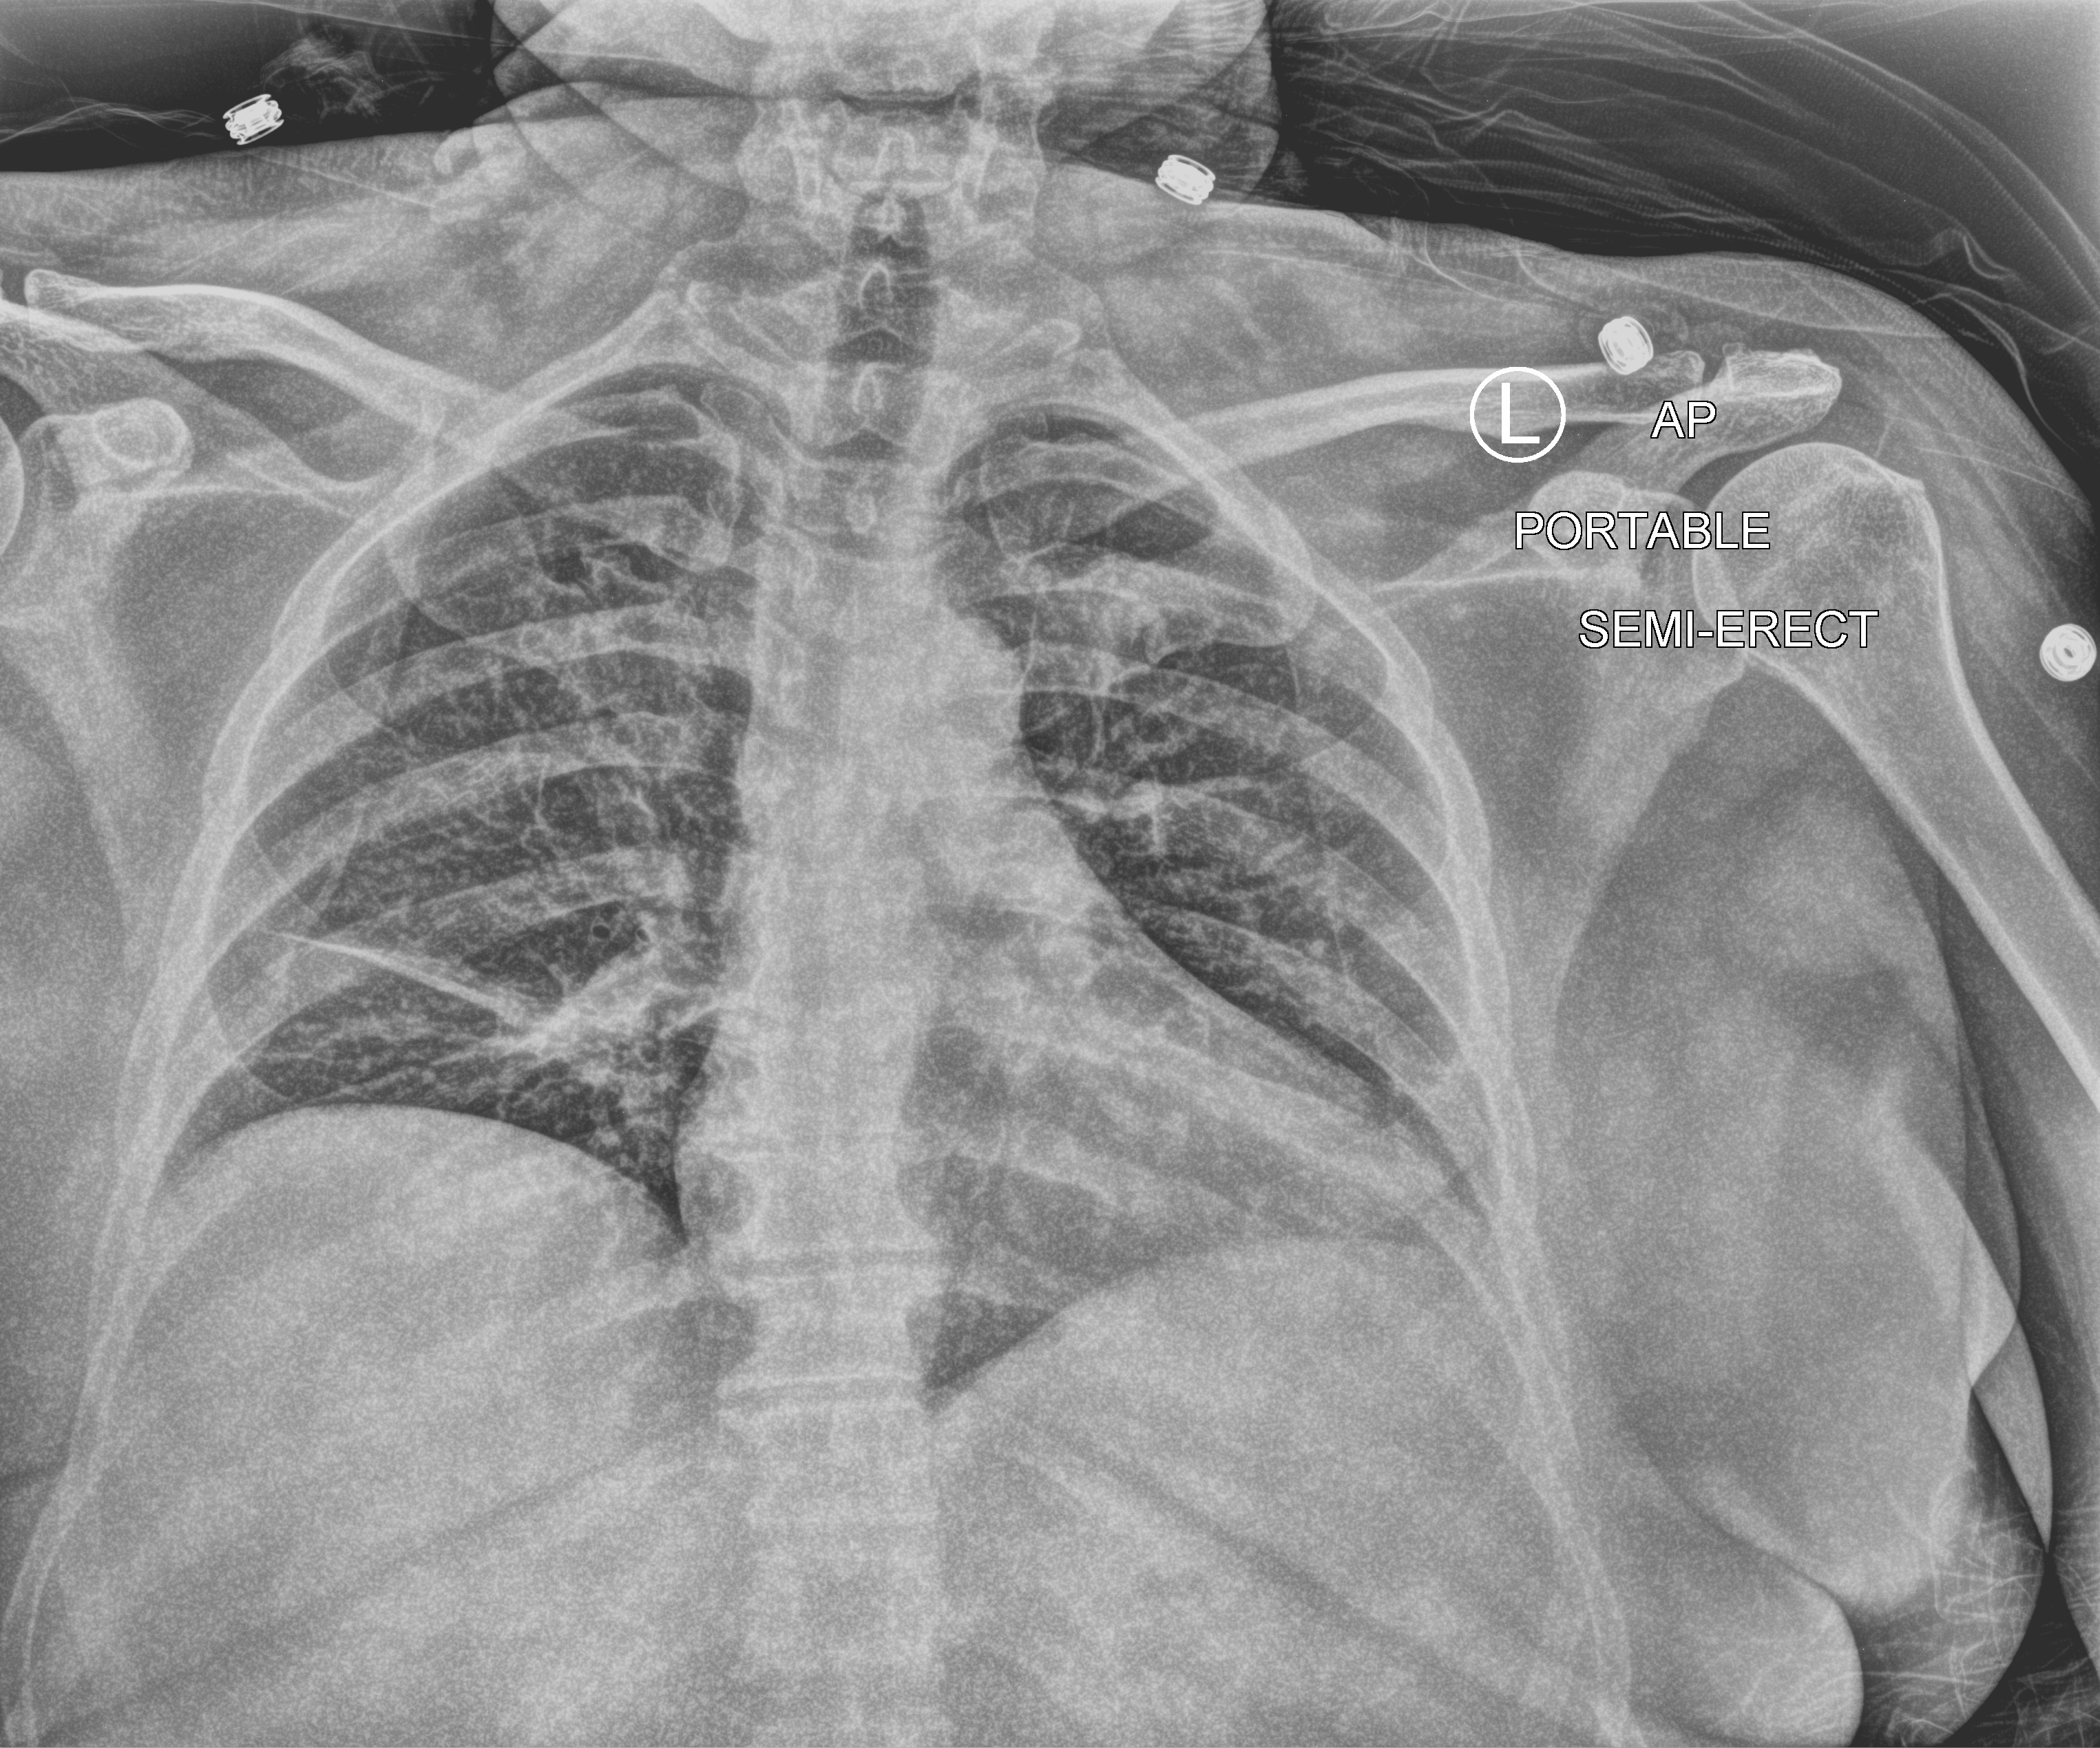
Portable chest radiograph. Patient hospitalised with COVID-19; female, aged 60–74 years.
Hospital-stay facts (about this admission, not read from this image; timing relative to this image not recorded):
- admitted to intensive care during this hospital stay: yes